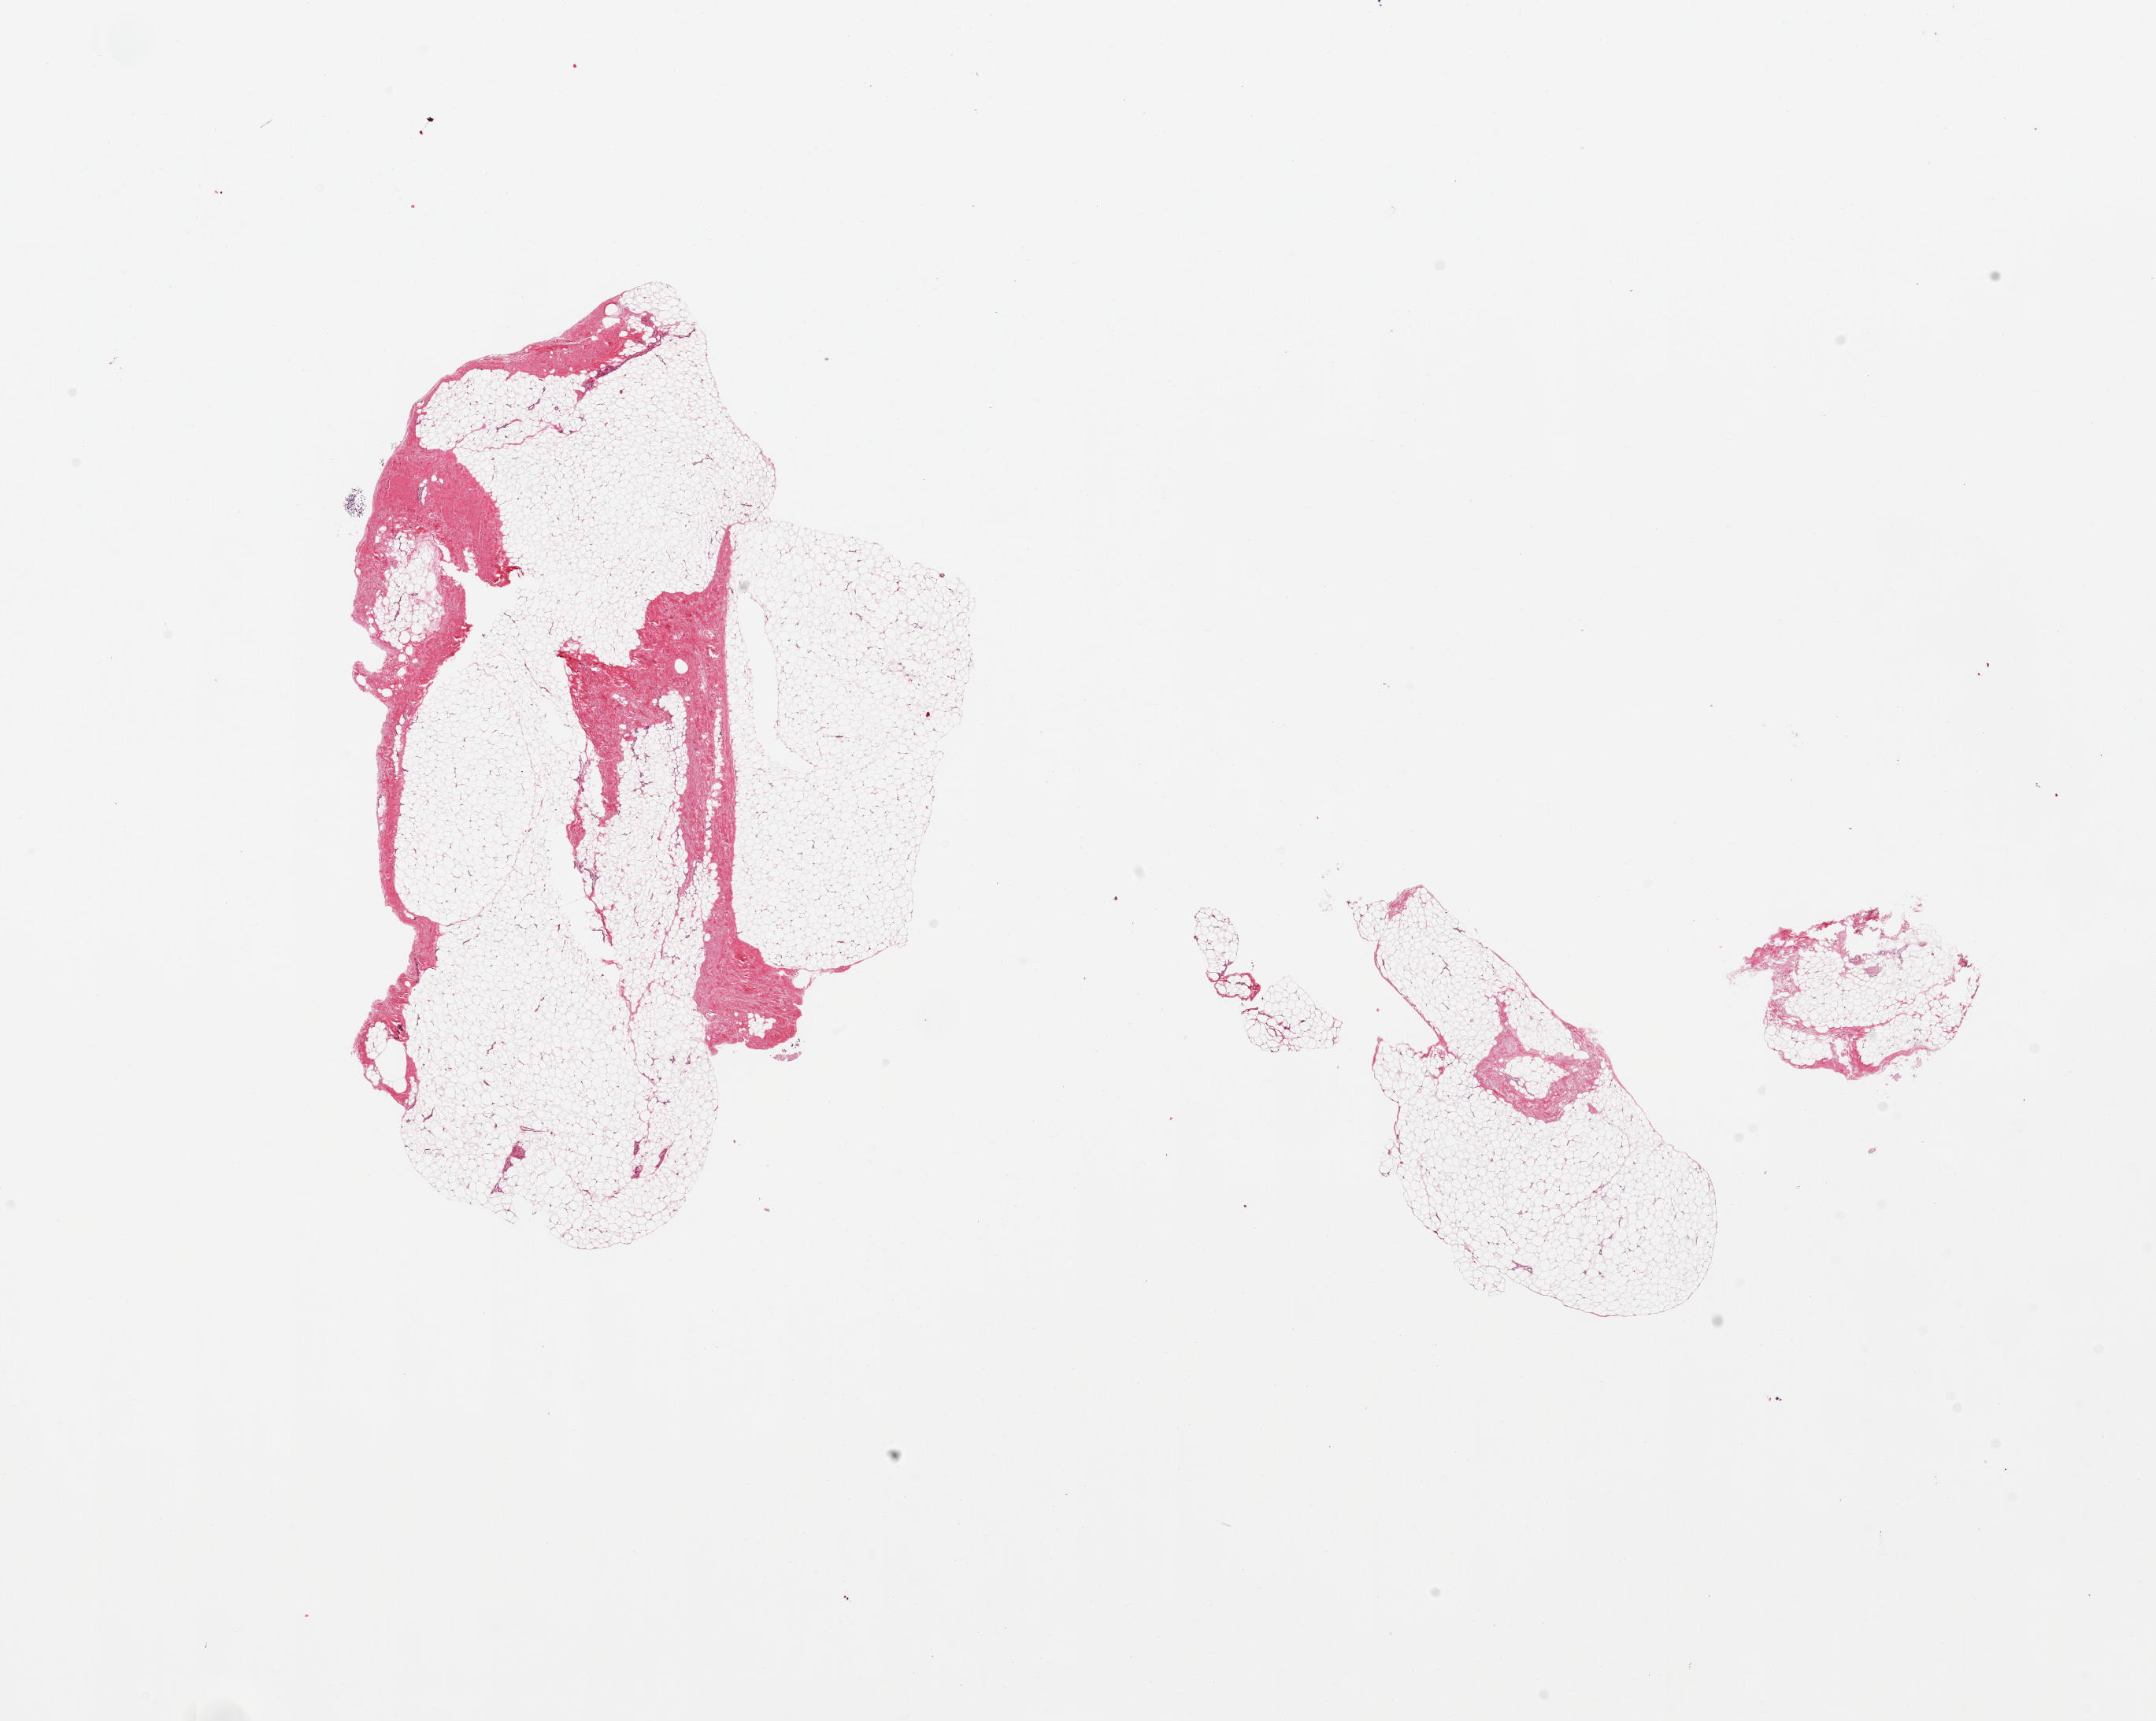
Digitized H&E-stained section — low-resolution overview of the scanned area, about 21.7 x 17.3 mm (slide scanned at 20x), PAXgene-fixed, paraffin-embedded tissue, section of adipose tissue (target tissue), donor tissue sample. Donor: male.
Reviewer comment on this tissue sample: 4 fragmented pieces; 10% fibrous content.